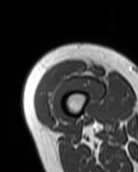
MRI of an extremity soft-tissue mass, one axial slice; position 10 of 99 along the scan axis; MR volume resampled by the dataset authors to the PET/CT grid (not the native acquisition matrix); 138 × 172 image matrix, field of view 135 × 168 mm. Female patient. Case-level facts recorded for this patient, not image findings: histological type: pleiomorphic undifferentiated sarcoma; grade: high; site of the primary tumour: right quadricep.
Structures marked on this image (expert contour drawn on MRI and transferred to this co-registered scan by the dataset authors):
- gross tumour volume including surrounding oedema: bounding box (x1, y1, x2, y2) in pixels: (37, 61, 86, 113)